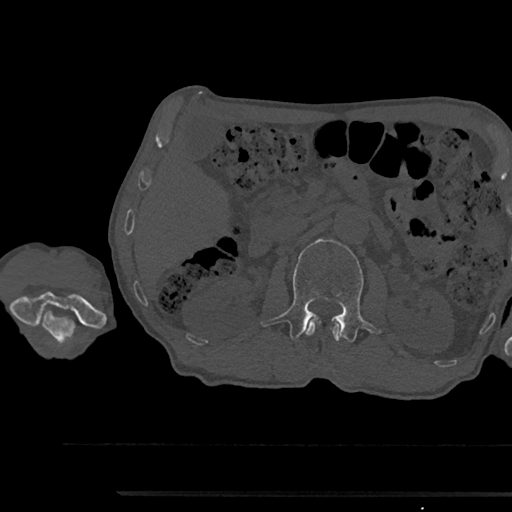
CT including the spine, one axial slice. Position 585 of 797 along the scan axis. Reconstruction kernel Br40s/3. 120 kVp. Bone window (W 1800 / L 400 HU). 512 × 512 image matrix. Male patient, age 79 years. Case-level facts recorded for this patient, not image findings: primary cancer: prostate.
Structures marked on this image (semi-automatically segmented with operator editing):
- L1 vertebra: bounding box (x1, y1, x2, y2) in pixels: (305, 318, 342, 342)
- L2 vertebra: (260, 239, 379, 342)